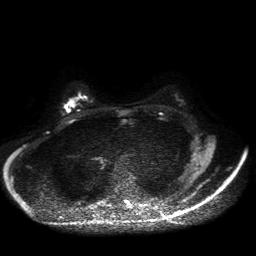
Breast MRI, one axial slice. Position 30 of 50 along the scan axis. Diffusion-weighted series; image 2 of 4 stored at this slice position (different b-values; order by instance number). 1.5 T. 4 mm slice thickness. 256 × 256 image matrix, field of view 360 × 360 mm. Female patient.
Outlined on this slice (expert manual segmentation):
- tumour on diffusion-weighted imaging: bounding box [x1, y1, x2, y2] px = [65, 100, 75, 112]